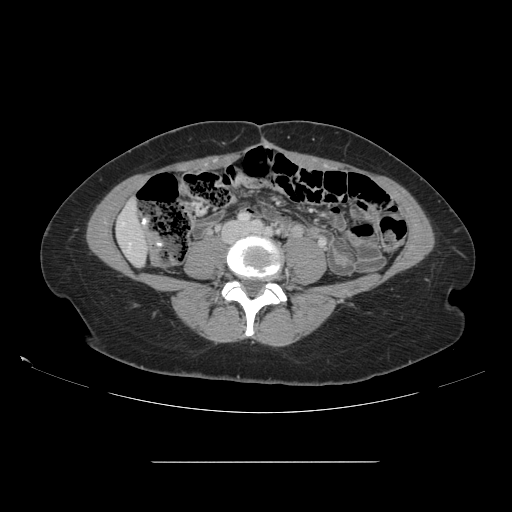
Contrast-enhanced abdominal CT, one axial slice. Intravenous contrast given. Soft-tissue window (W 400 / L 40 HU). 2.5 mm slice thickness. 512 × 512 image matrix, field of view 421 × 421 mm. Female patient, age 46 years. Case-level facts recorded for this patient, not image findings: diagnosis: colorectal cancer liver metastases, imaged before liver resection; multiple liver metastases: yes; largest metastasis: 3 cm; disease in both lobes: yes.
Structures marked on this image (manually delineated by an expert):
- liver: bounding box <118,202,148,265> (left, top, right, bottom; pixels)
- planned liver remnant (the part of the liver to remain after resection): <117,202,148,265>